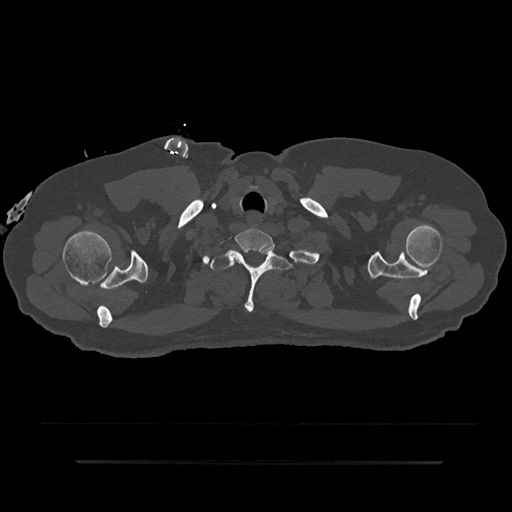
CT including the spine, one axial slice; slice 749 of 797 in the series (ordered by position); reconstruction kernel Br40s/3; 120 kVp; bone window (W 1800 / L 400 HU); 0.5 mm slice thickness; 512 × 512 image matrix, field of view 464 × 464 mm. Male patient, age 59 years. From the clinical record (not read from this slice): primary cancer: bile ducts; vertebrae with lytic lesions (as recorded): T10.
Annotated regions visible in this slice (semi-automatic segmentation, software-assisted and operator-edited):
- T1 vertebra: bounding box (x1, y1, x2, y2) in pixels: (210, 247, 291, 312)